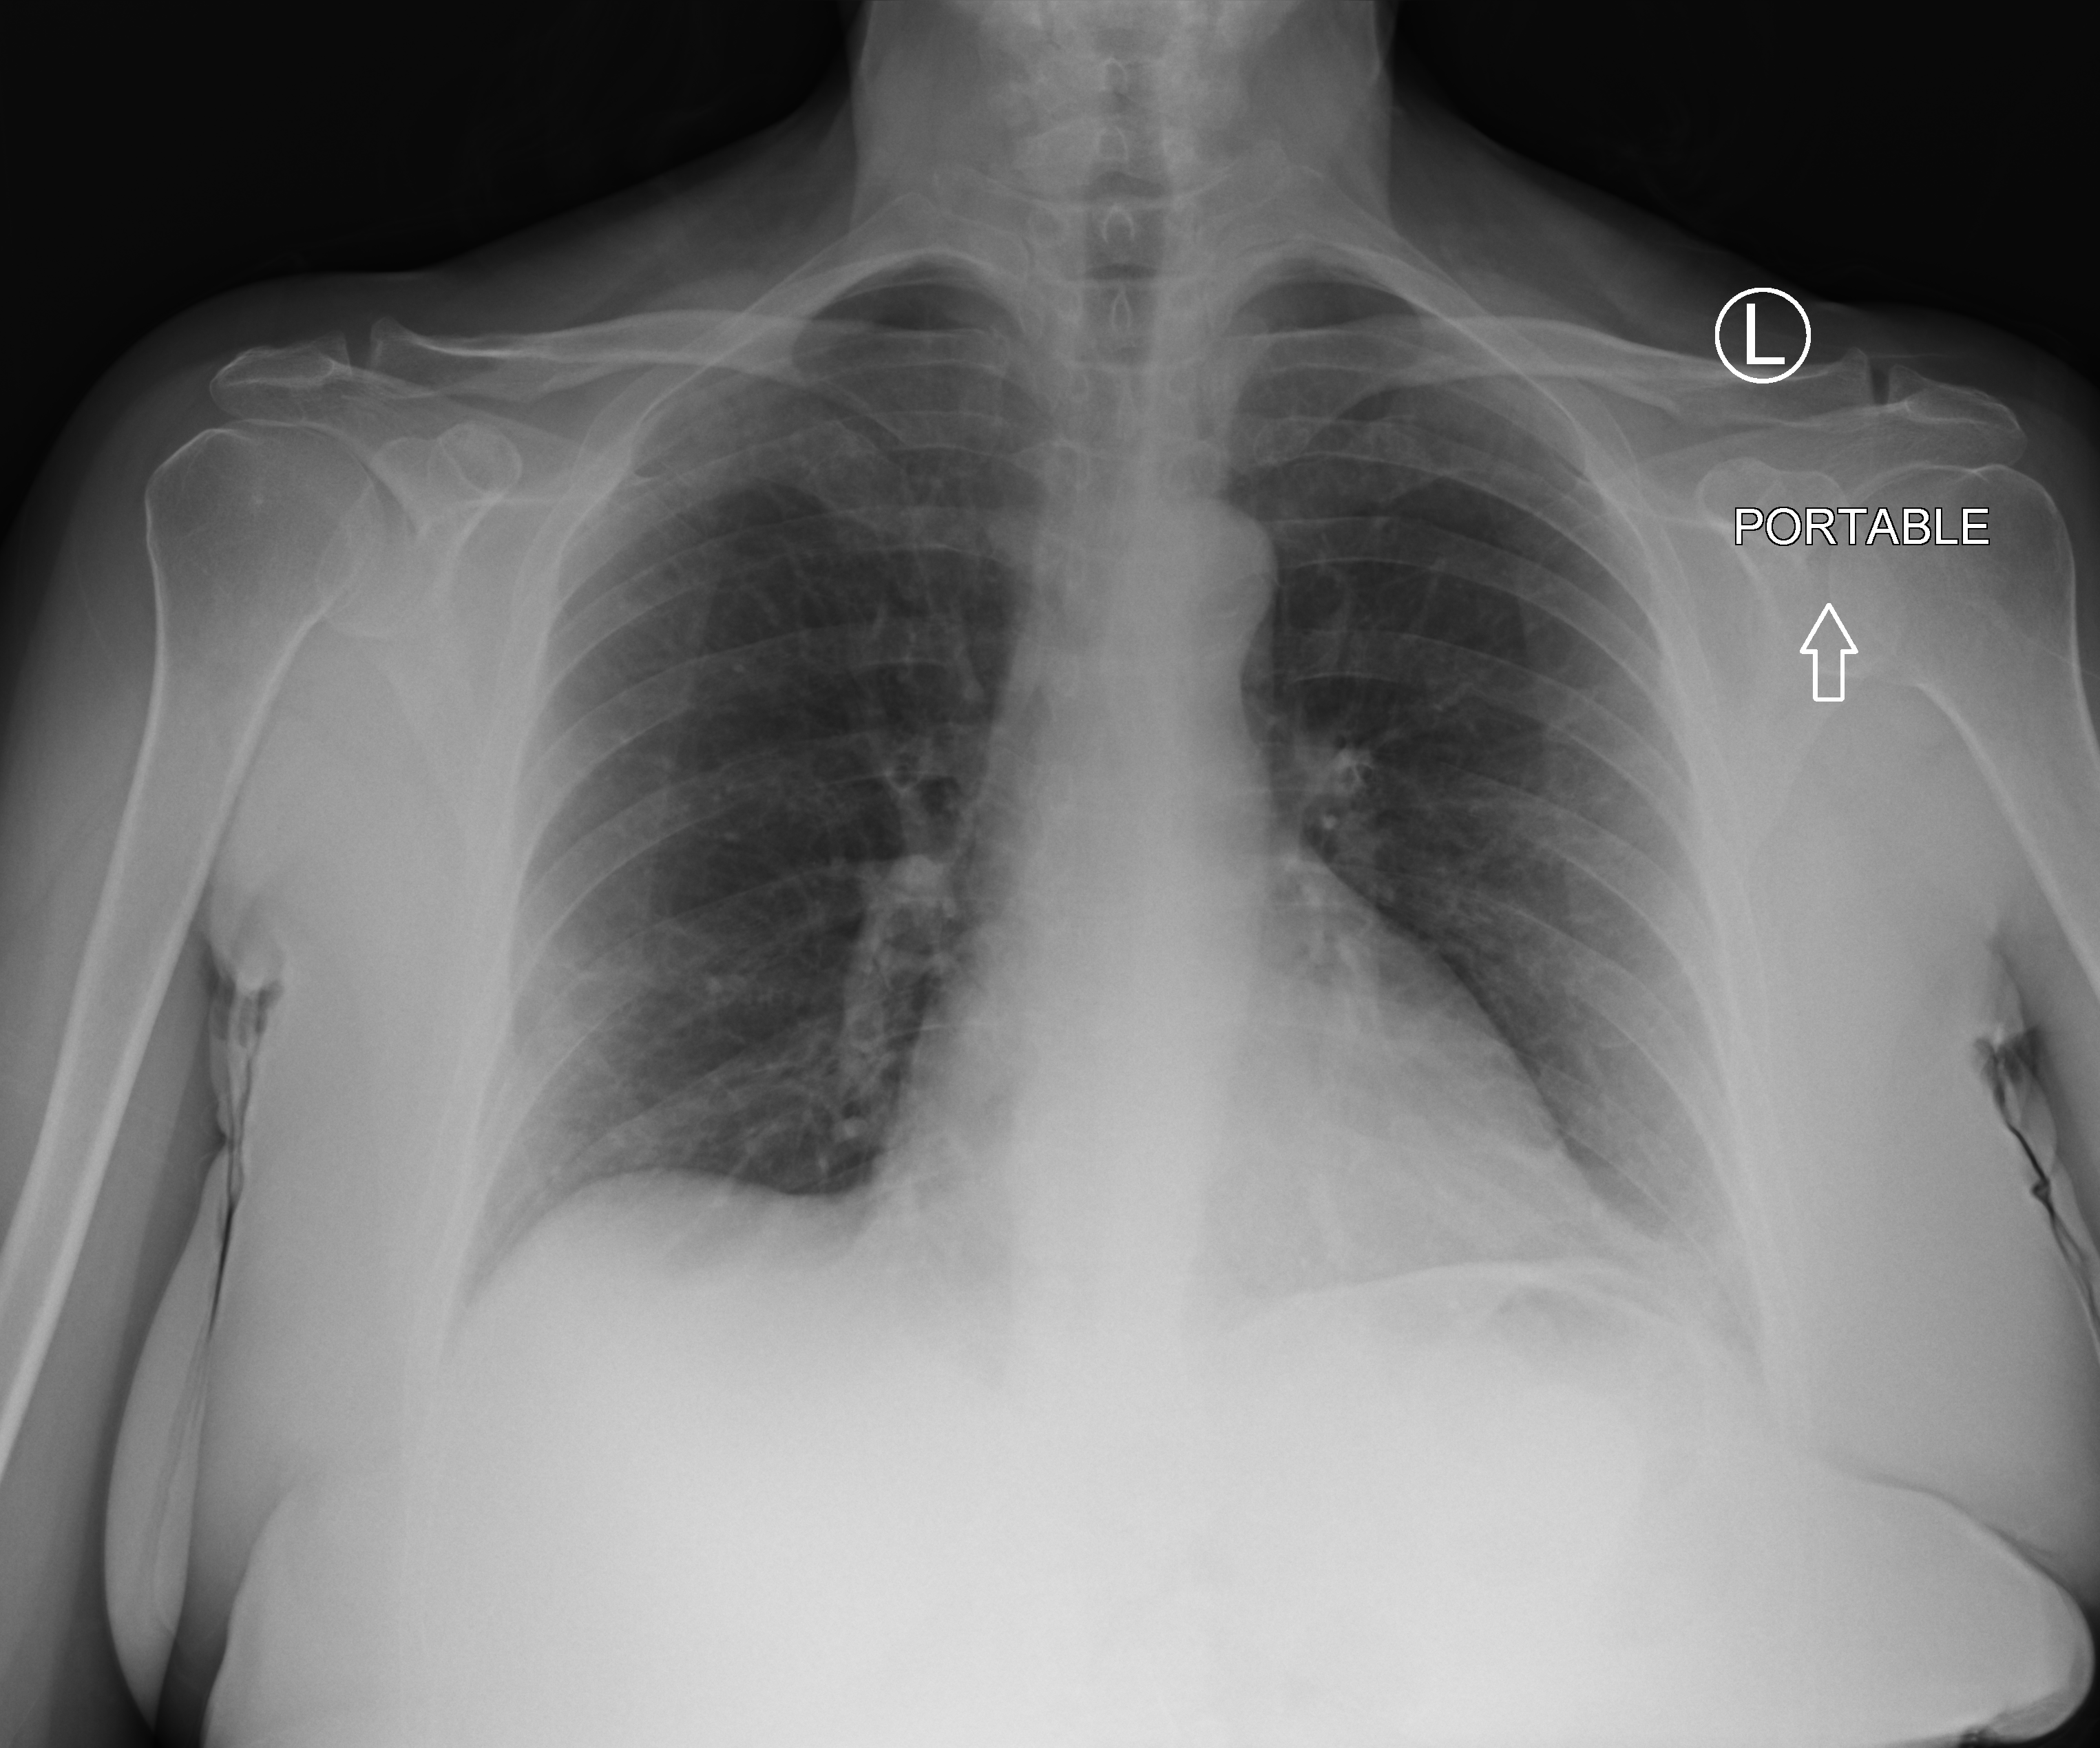
Portable chest radiograph. Female patient hospitalised with COVID-19, age 60–74 years.
From the hospital-stay record, not from the radiograph (when in the stay this image was taken is not recorded):
- admitted to intensive care during this hospital stay: no
- other chronic lung disease (admission record): no